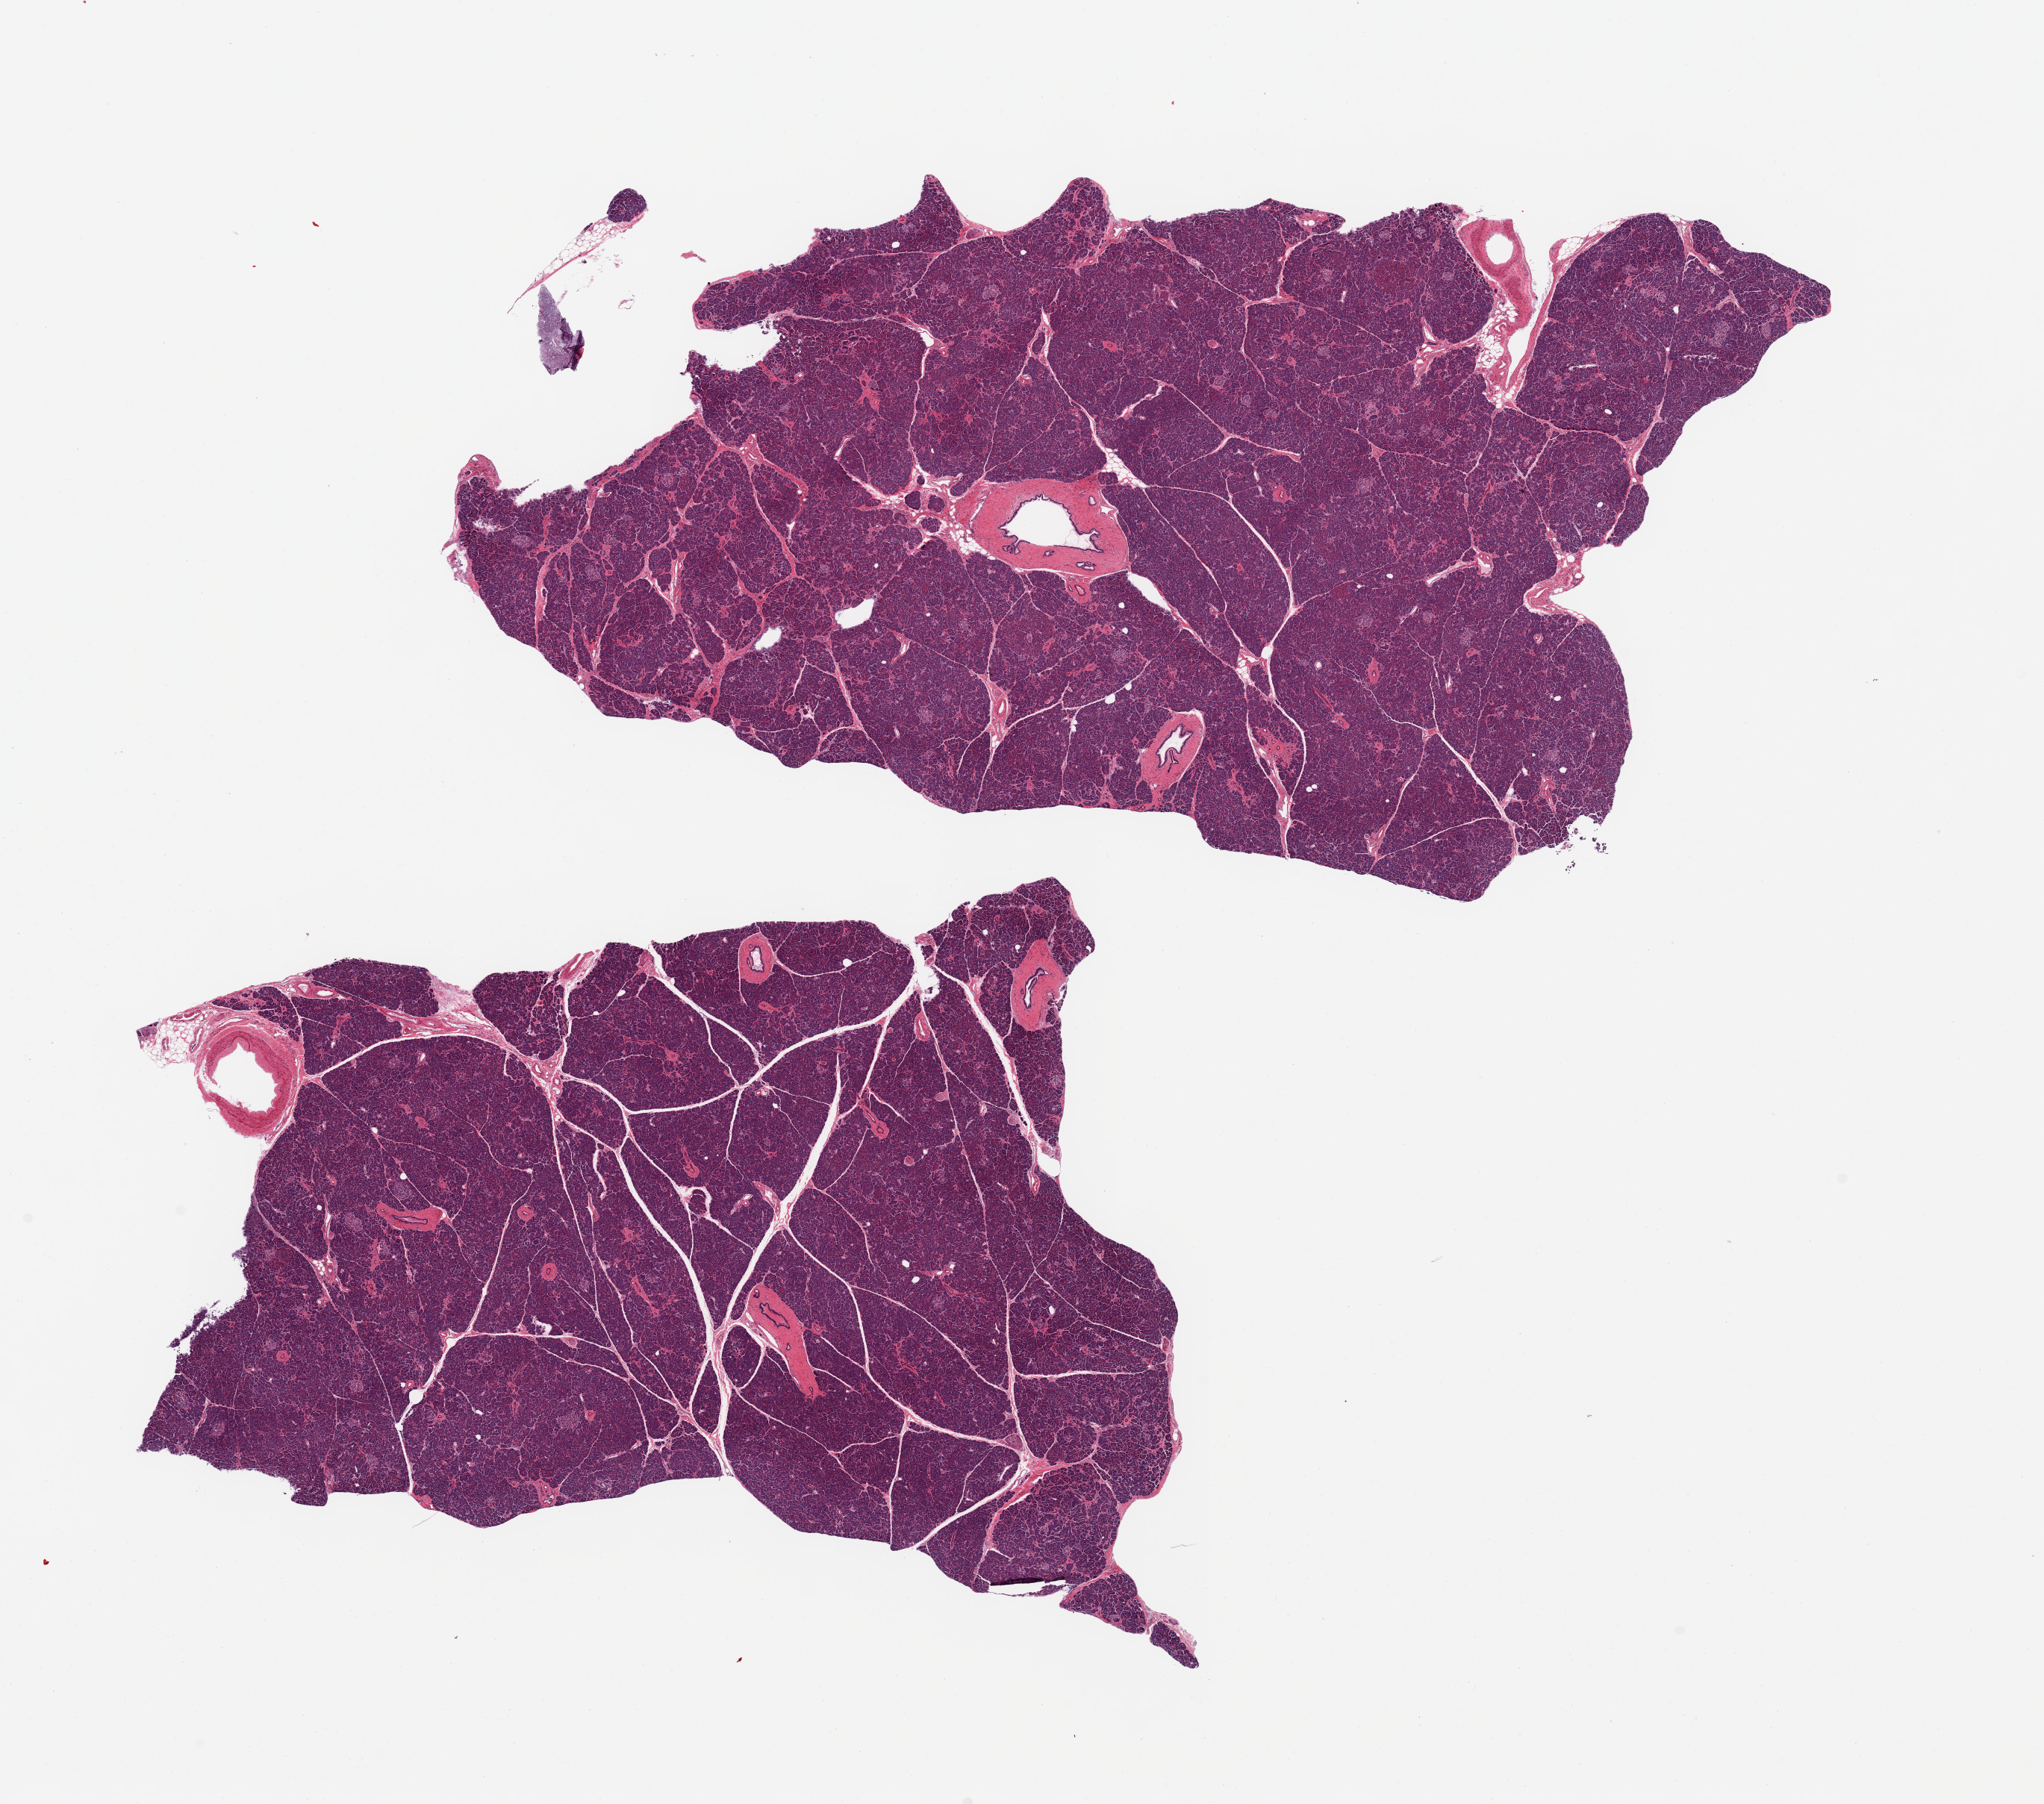
Hematoxylin and eosin (H&E) whole-slide image, brightfield — low-resolution overview of the scanned area, about 21.7 x 19.1 mm, PAXgene-fixed, paraffin-embedded tissue, target tissue: pancreas, tissue donor sample. Donor: female.
Pathologist's review note for this sample: 2 pieces, well preserved, minimal fat; Islets well visualized.